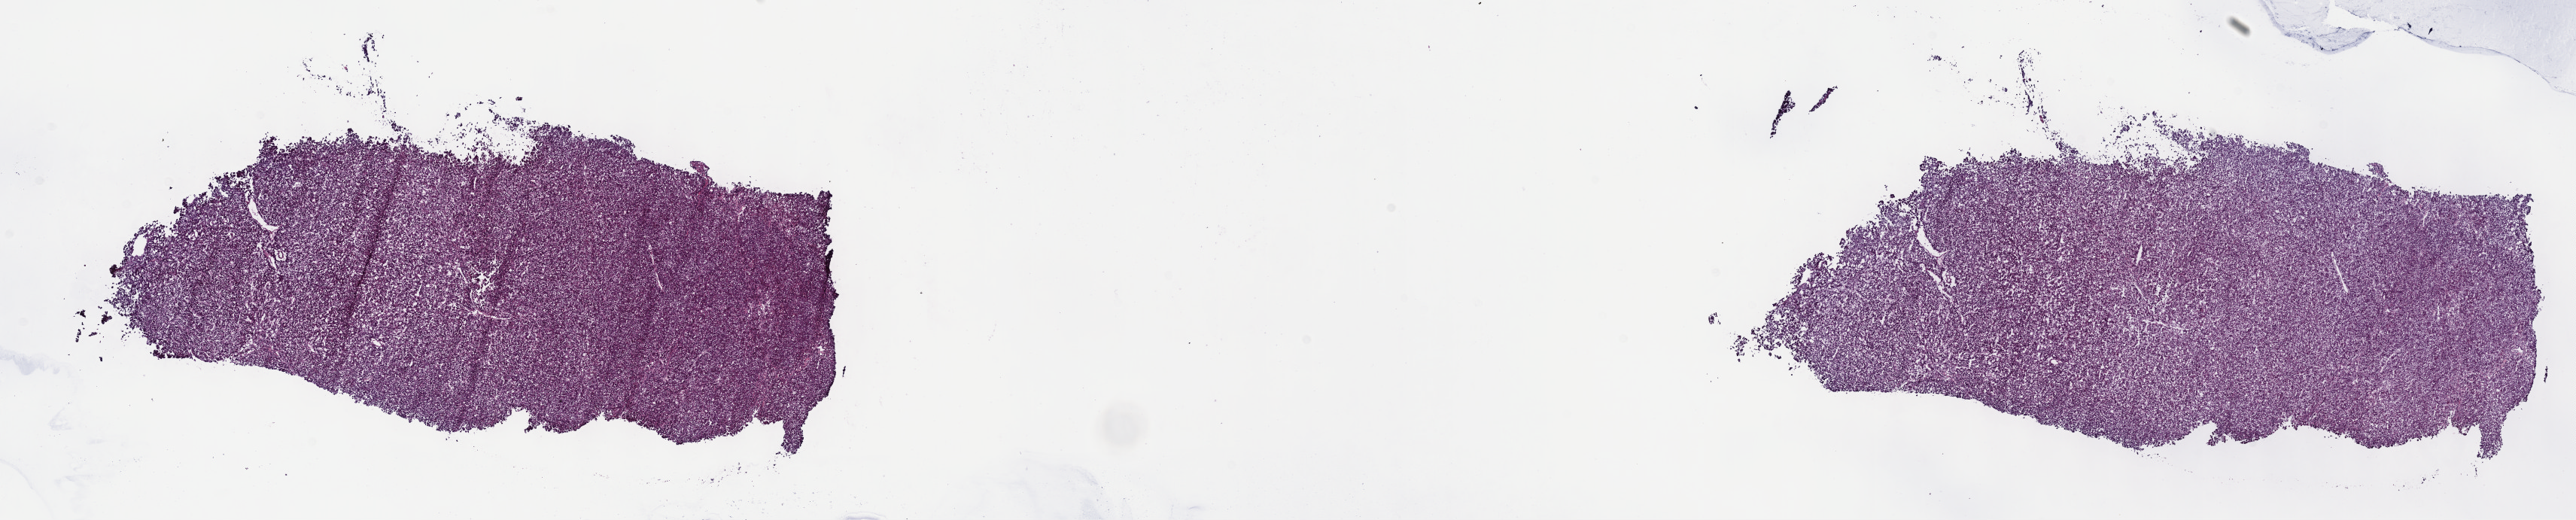
Digitized H&E tissue section (whole slide) — a low-resolution overview of the entire scanned area, about 27.7 x 5.6 mm (slide scanned at 40x). Frozen section from the top of the tissue portion. Liver, primary tumour sample. Male patient; age at initial diagnosis 67 years. Histologic grade: G2 (moderately differentiated). Slide review estimates, as recorded: tumour cells 100%, tumour nuclei 80%, normal cells 0%, stromal cells 0%, necrosis 0%. Infiltration values recorded for this section: lymphocyte infiltration 2%, monocyte infiltration 0%, neutrophil infiltration 0%.
• histologic diagnosis: Hepatocellular carcinoma, NOS
• AJCC pathologic stage: II (7th edition)